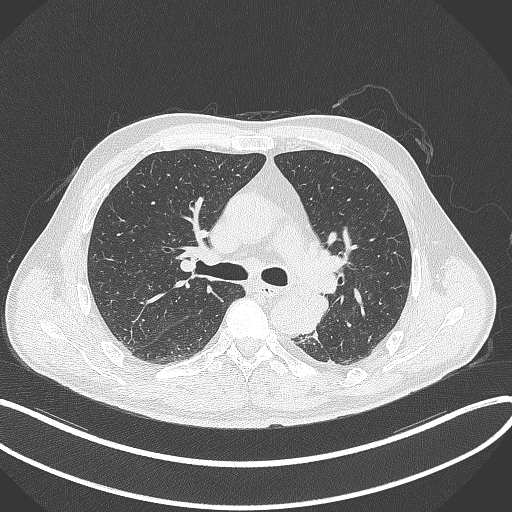
Chest CT, one axial slice; slice 218 of 329 in the series (ordered by position); reconstruction kernel B70f; 120 kVp; lung window (W 1500 / L -600 HU); 1 mm slice thickness; 512 × 512 image matrix, field of view 400 × 400 mm. Male patient, age 59 years. From the clinical record (not read from this slice): clinical TNM (as recorded): T2a N2 M0.
Annotated regions visible in this slice (bounding box drawn by a radiologist):
- lung tumour (recorded histology: squamous cell carcinoma): bounding box (x1, y1, x2, y2) in pixels: (306, 292, 330, 323)